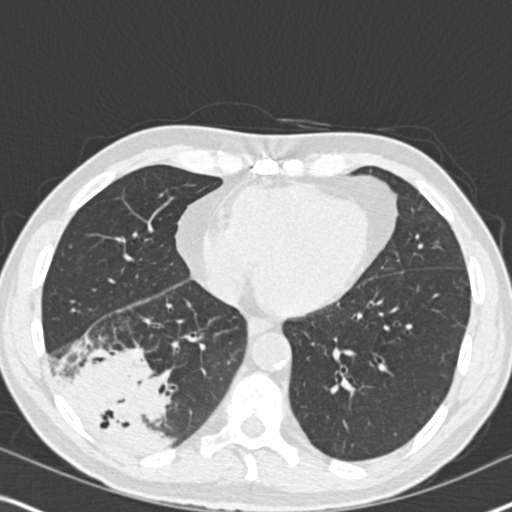
Low-dose screening chest CT, one axial slice; slice 71 of 182 in the series (ordered by position); reconstruction kernel B30f; lung window (W 1500 / L -600 HU); 2 mm slice thickness; 512 × 512 image matrix, field of view 330 × 330 mm.
Outlined on this slice (expert manual segmentation):
- lesion 1 (tumor, lower lobe of right lung): box from (x=62, y=346) to (x=169, y=455) px